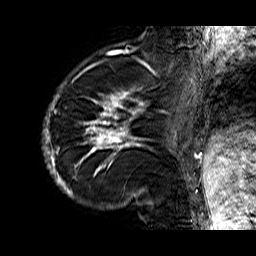
Breast MRI (dynamic contrast-enhanced), one sagittal slice; slice 12 of 60 in the series (ordered by position); dynamic contrast-enhanced series, time point 2 of 6 at this slice position (early post-contrast); 1.5 T; TE 6.3 ms, TR 32.9 ms; 4 mm slice thickness; 256 × 256 image matrix. Female patient. From the clinical record (not read from this slice): setting: breast cancer imaged before/during neoadjuvant chemotherapy; receptor status: HR-positive, HER2-negative.
Structures marked on this image (semi-automatic segmentation, software-assisted and operator-edited):
- analysis volume of interest (the breast-tissue region the enhancement analysis was run in; not a lesion): bounding box <43,74,176,210> (left, top, right, bottom; pixels)
- tumour enhancement mask (voxels above the 100 % enhancement threshold inside the analysis volume of interest): <43,82,176,204>